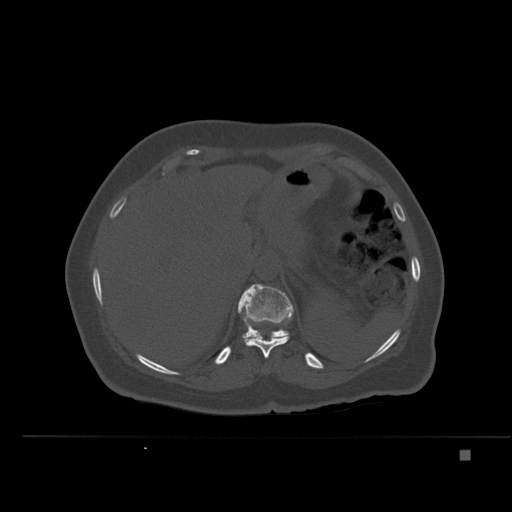
CT including the spine, one axial slice. Slice 264 of 477 in the series (ordered by position). Bone window (W 1800 / L 400 HU). 1.5 mm slice thickness. 512 × 512 image matrix. Patient: female, 74 years. Case-level facts recorded for this patient, not image findings: primary cancer: colon.
Outlined on this slice (semi-automatic segmentation, software-assisted and operator-edited):
- T11 vertebra: bounding box [x1, y1, x2, y2] px = [244, 335, 289, 358]
- T12 vertebra: [238, 284, 294, 338]